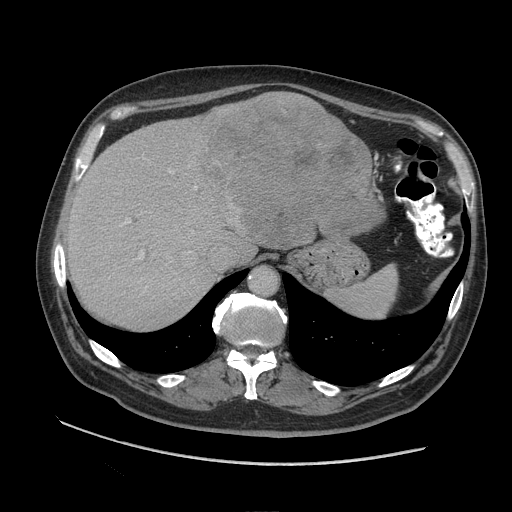
Contrast-enhanced abdominal CT (liver protocol), one axial slice. Position 72 of 109 along the scan axis. Reconstruction kernel STANDARD. 140 kVp. Soft-tissue window (W 400 / L 40 HU). 512 × 512 image matrix, field of view 420 × 420 mm. Case-level facts recorded for this patient, not image findings: diagnosis: hepatocellular carcinoma (patient treated with transarterial chemoembolisation; whether this scan precedes or follows treatment is not stated here); TNM stage (as recorded): Stage-I; Child-Pugh class: A.
Outlined on this slice (semi-automatic segmentation, software-assisted and operator-edited):
- abdominal aorta: bounding box (x1, y1, x2, y2) in pixels: (250, 268, 277, 296)
- liver parenchyma outside the tumour (the mass and vessels are separate outlines, so this box may not span the whole liver): (66, 92, 323, 328)
- mass: (197, 91, 387, 248)
- liver vessels: (120, 158, 197, 288)